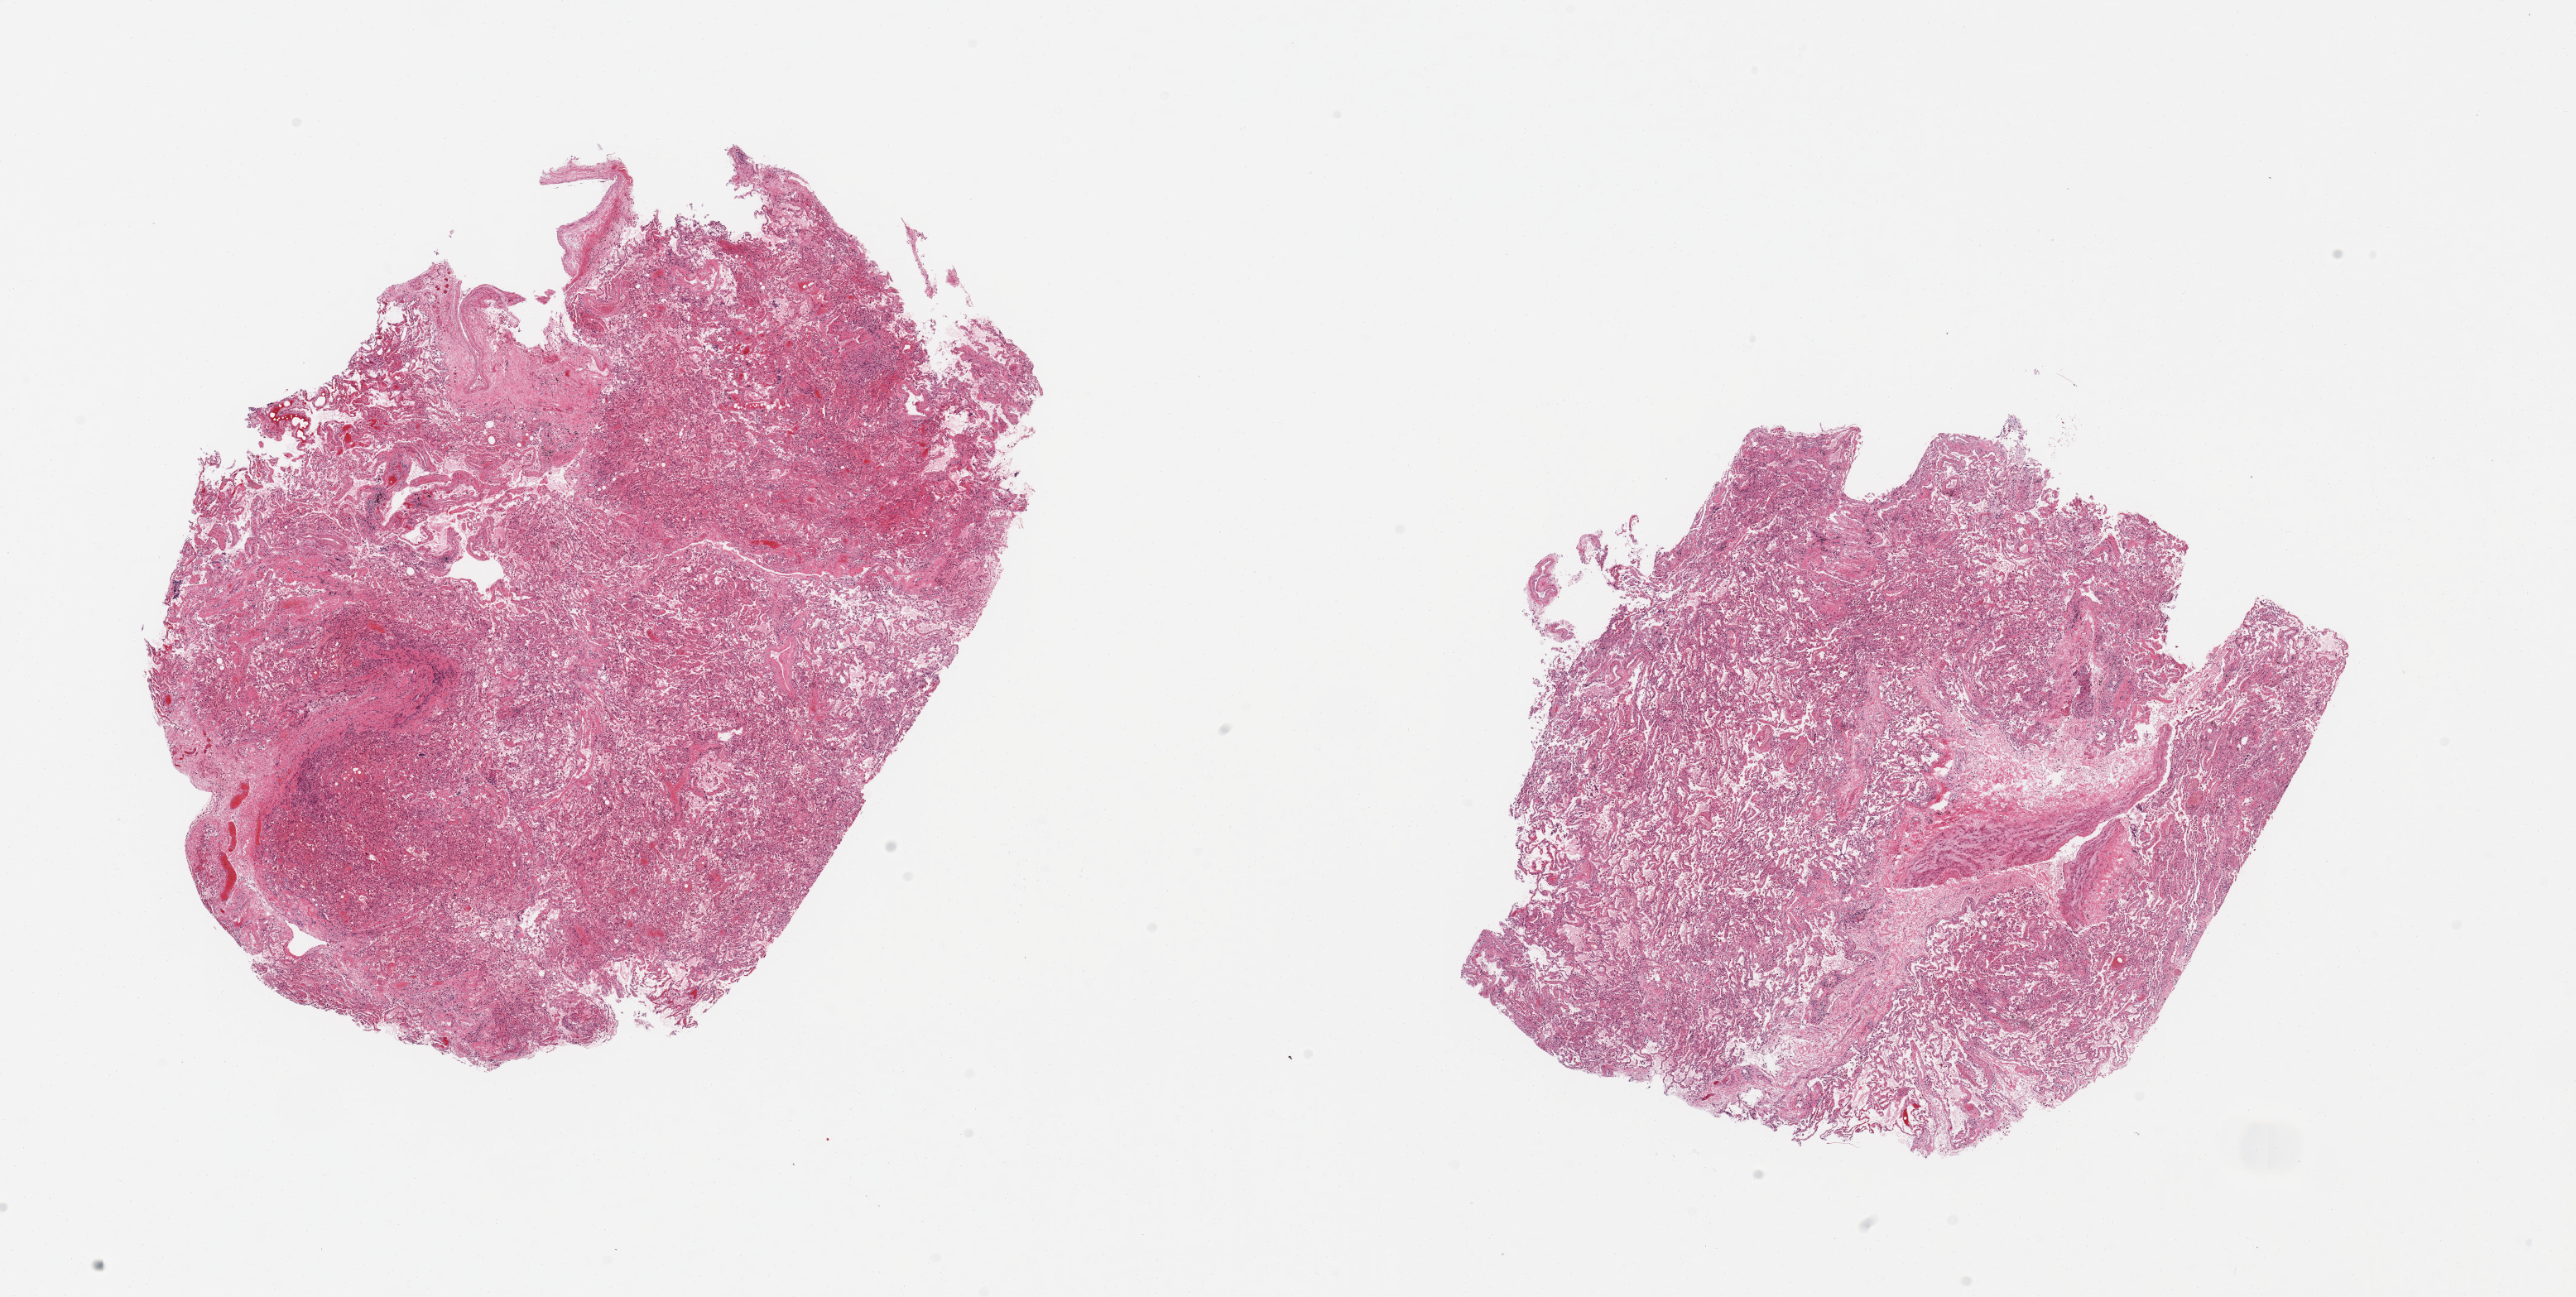
Whole-slide image, haematoxylin and eosin stain — shown as a low-resolution overview of the whole scanned area (about 24.6 x 12.4 mm), PAXgene-fixed, paraffin-embedded tissue, sampled site (target tissue): lung, donor tissue sample. Donor sex: female.
* reviewer comment on this tissue sample: 2 pieces, moderate congestion/edema